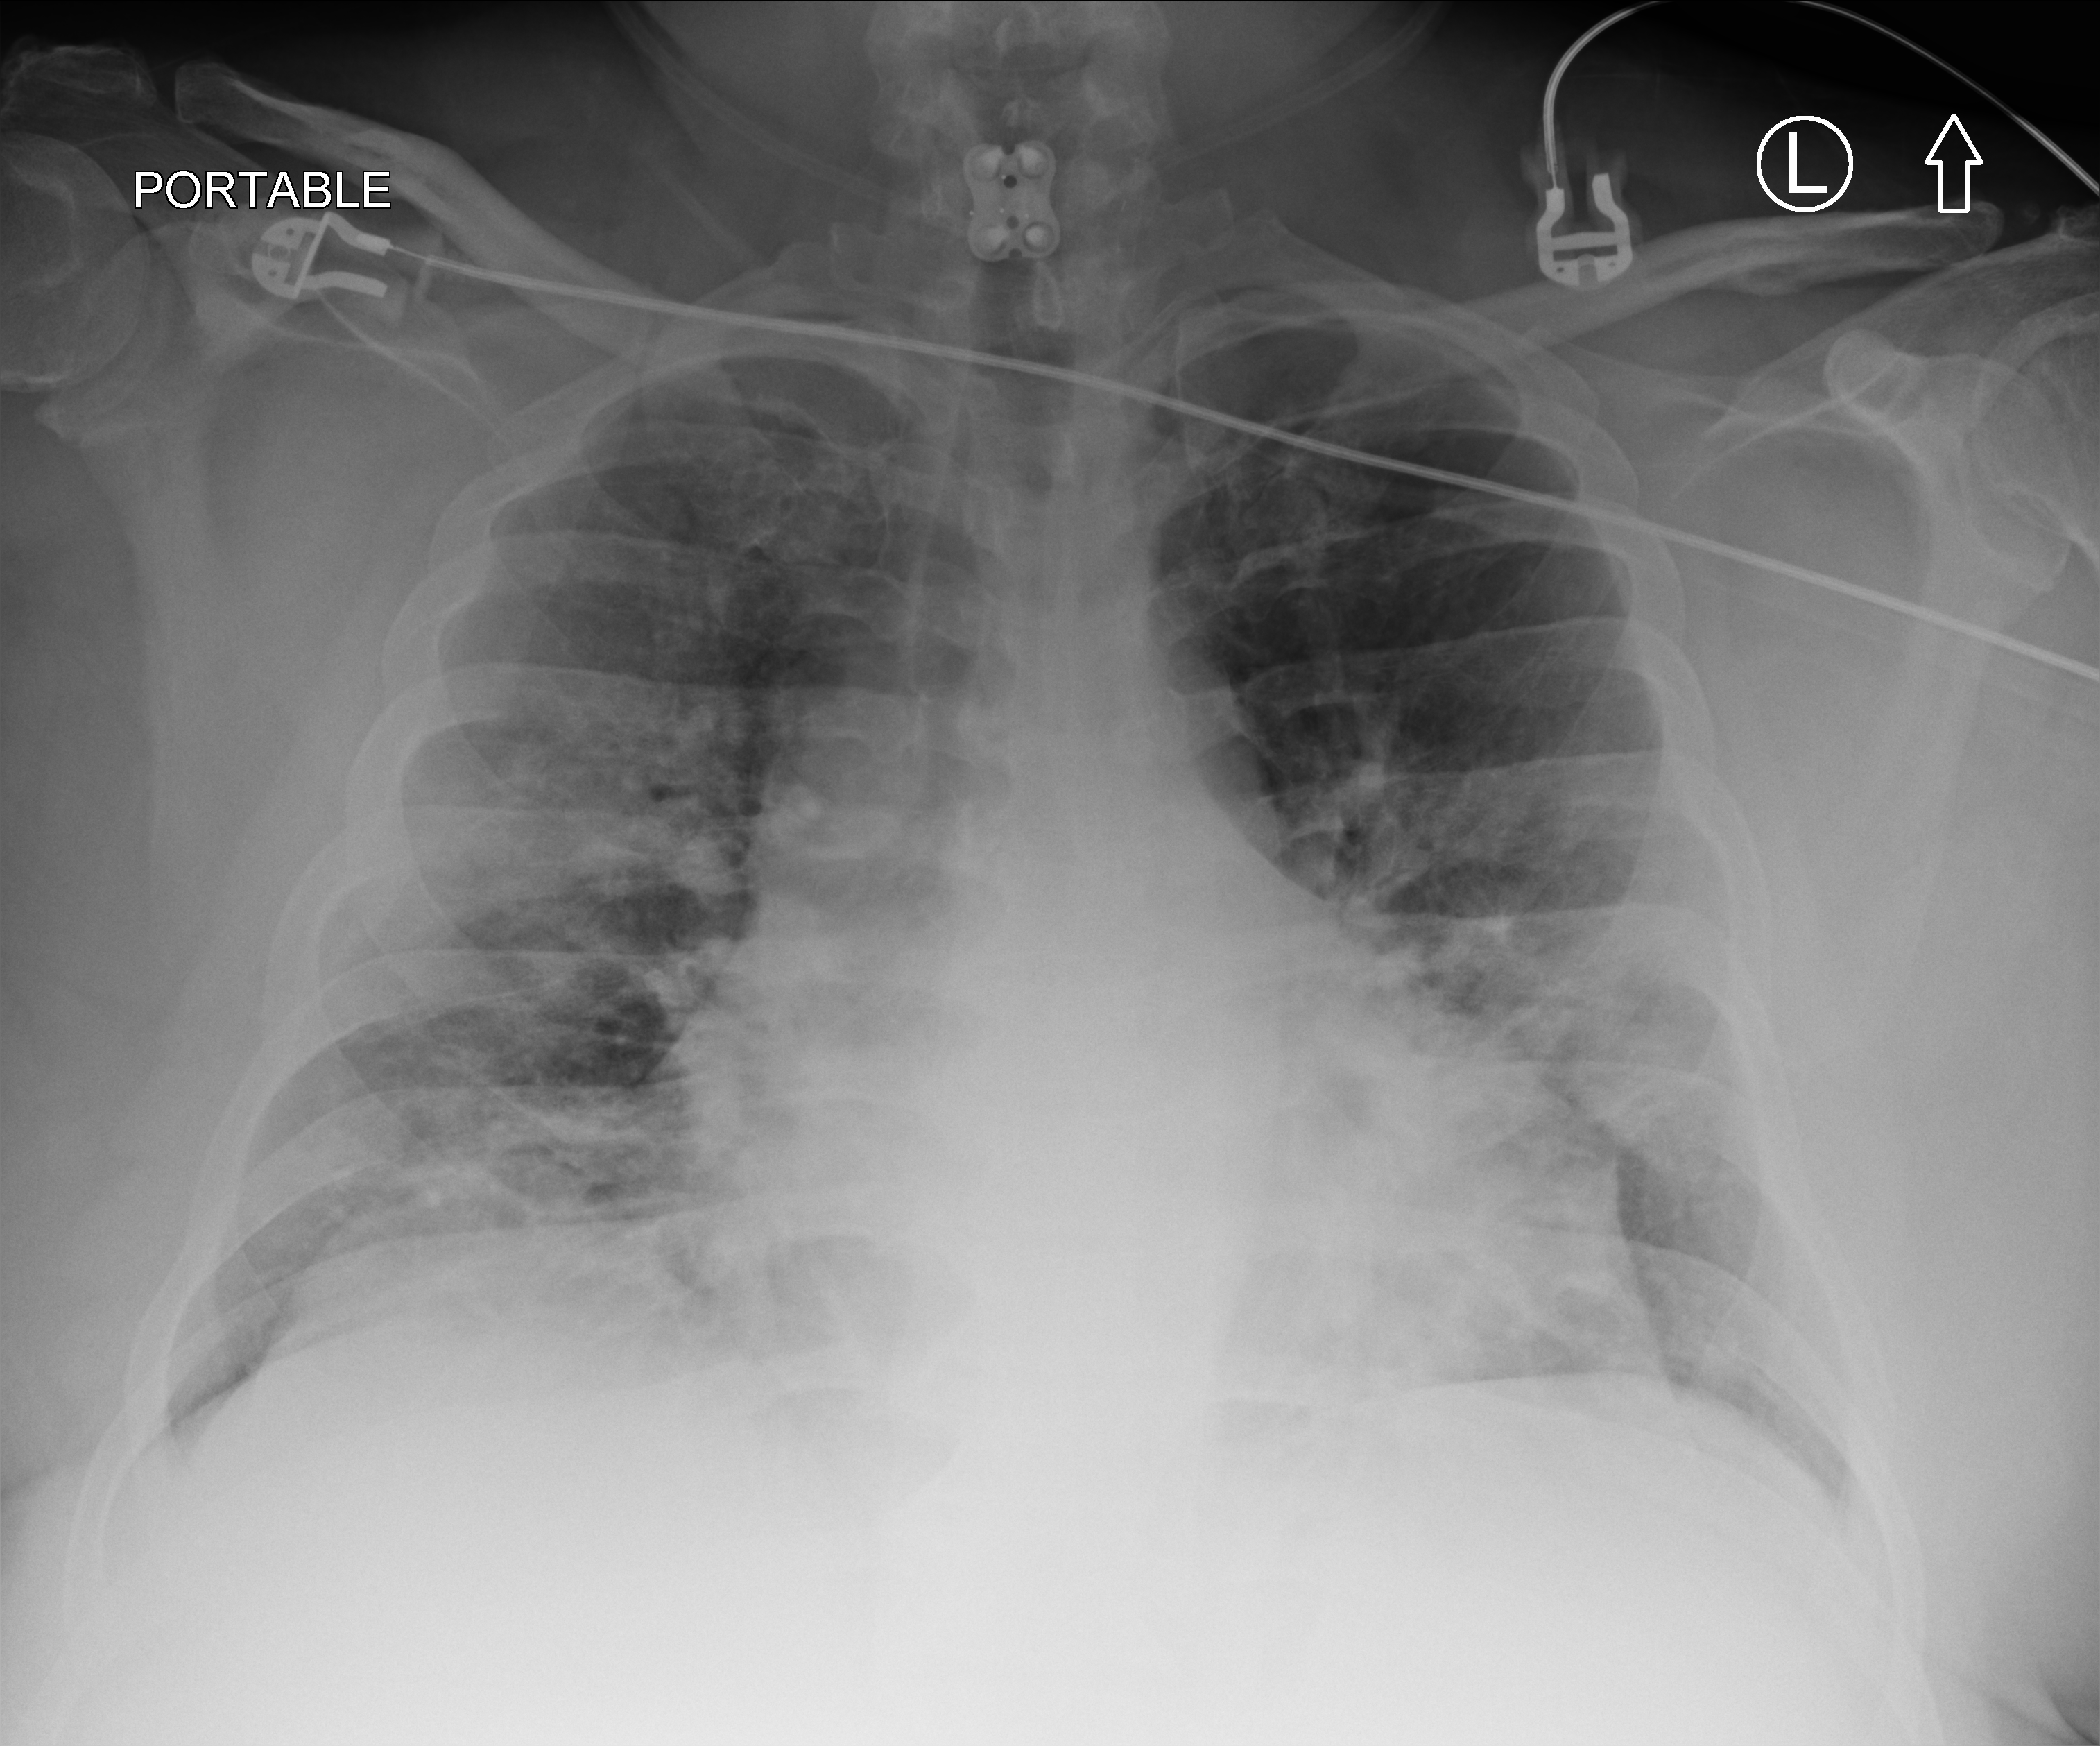
Chest X-ray (portable), anteroposterior (AP) projection. Male patient hospitalised with COVID-19, age 18–59 years.
From the hospital-stay record, not from the radiograph (when in the stay this image was taken is not recorded):
- COPD (admission record): no
- length of hospital stay: 47 days
- diabetes (admission record): no